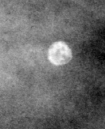
Region of interest cut from a scanned film mammogram (one marked finding), right breast, CC view, BI-RADS breast density category 3 (scale 1–4).
Marked abnormality: calcifications, morphology lucent center; BI-RADS assessment category 2; benign; no additional work-up was recommended (benign without callback).